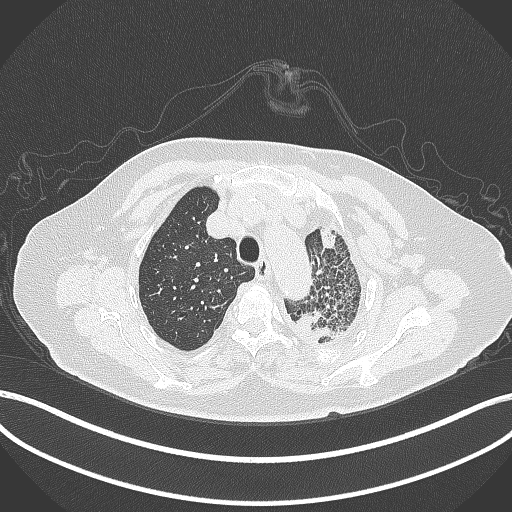
Chest CT, one axial slice; slice 317 of 399 in the series (ordered by position); reconstruction kernel B70f; lung window (W 1500 / L -600 HU); 512 × 512 image matrix. Patient: female, 75 years. Case-level facts recorded for this patient, not image findings: clinical TNM (as recorded): T3 N3 M1.
Structures marked on this image (rectangle marked by the reading radiologist):
- lung tumour (recorded histology: adenocarcinoma): bounding box [x1, y1, x2, y2] px = [287, 301, 340, 350]